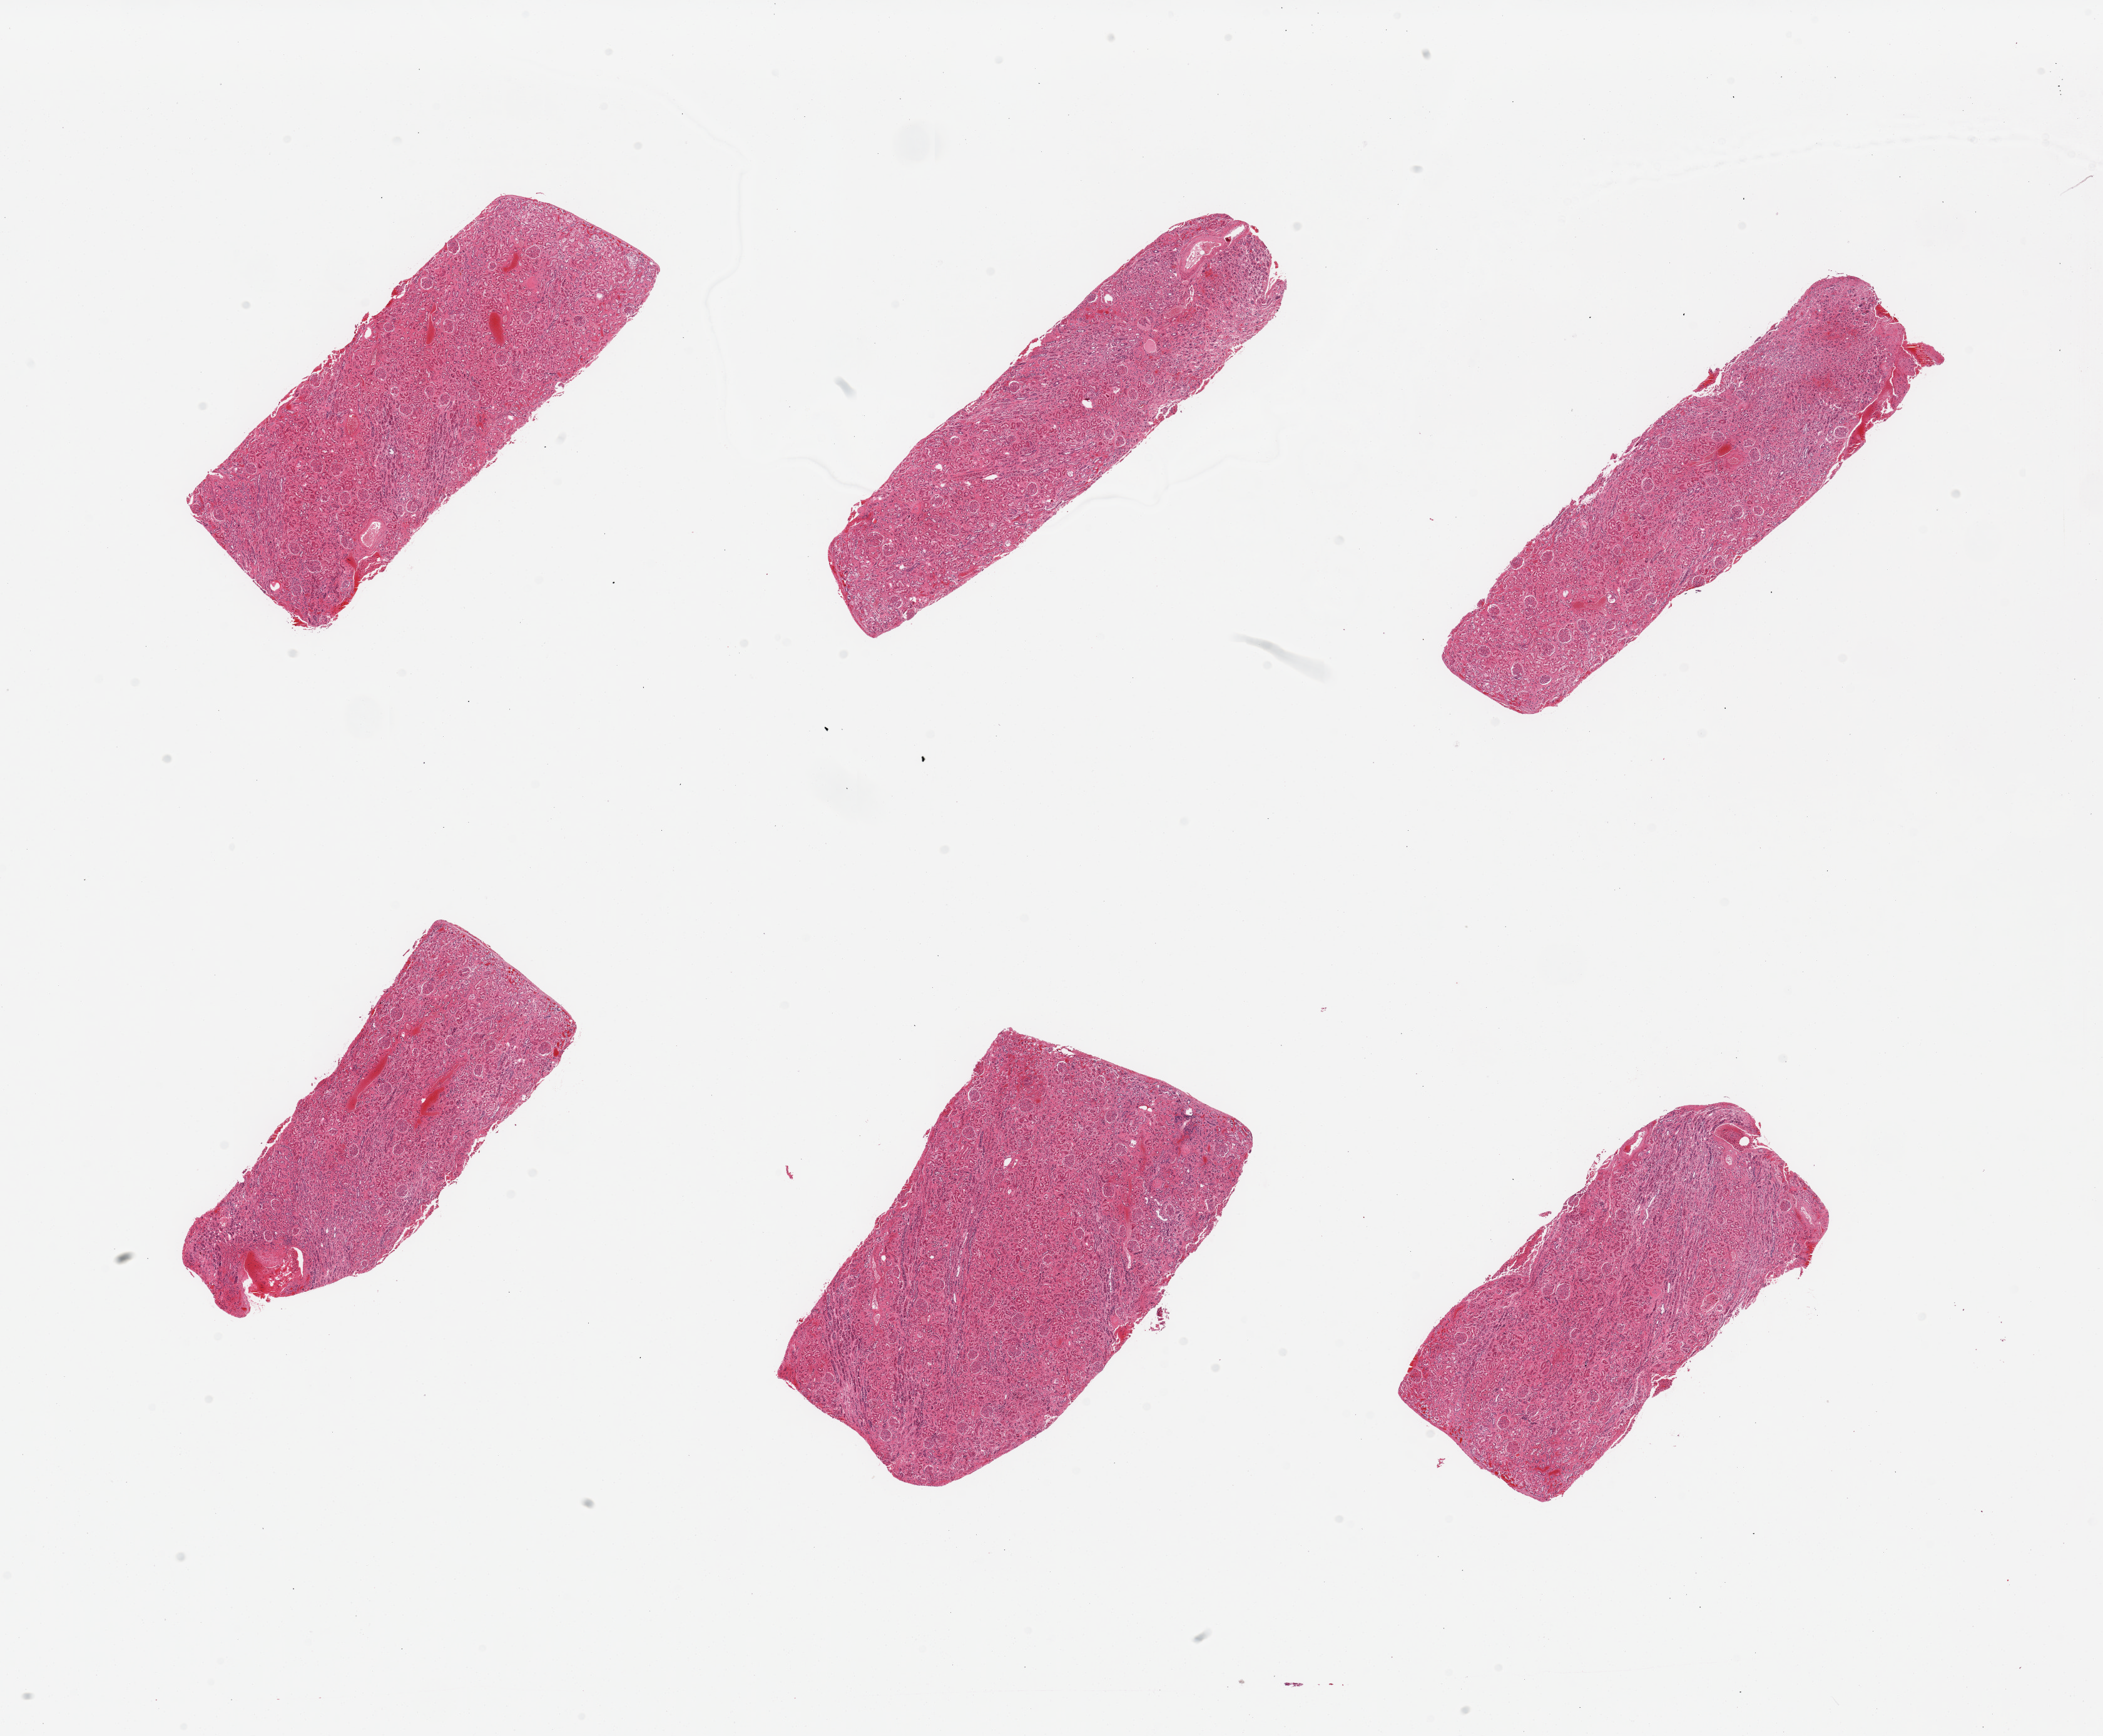
Hematoxylin and eosin (H&E) whole-slide image — whole scanned area (about 26.6 x 21.9 mm, slide scanned at 20x) shown as a low-resolution overview. PAXgene-fixed, paraffin-embedded tissue. Section of renal cortex (target tissue). Donor tissue sample. Donor: male.
Pathologist's review note for this sample: 6 pieces; predominantly renal cortex with rare sclerotic glomerulus, small portion of medulla.